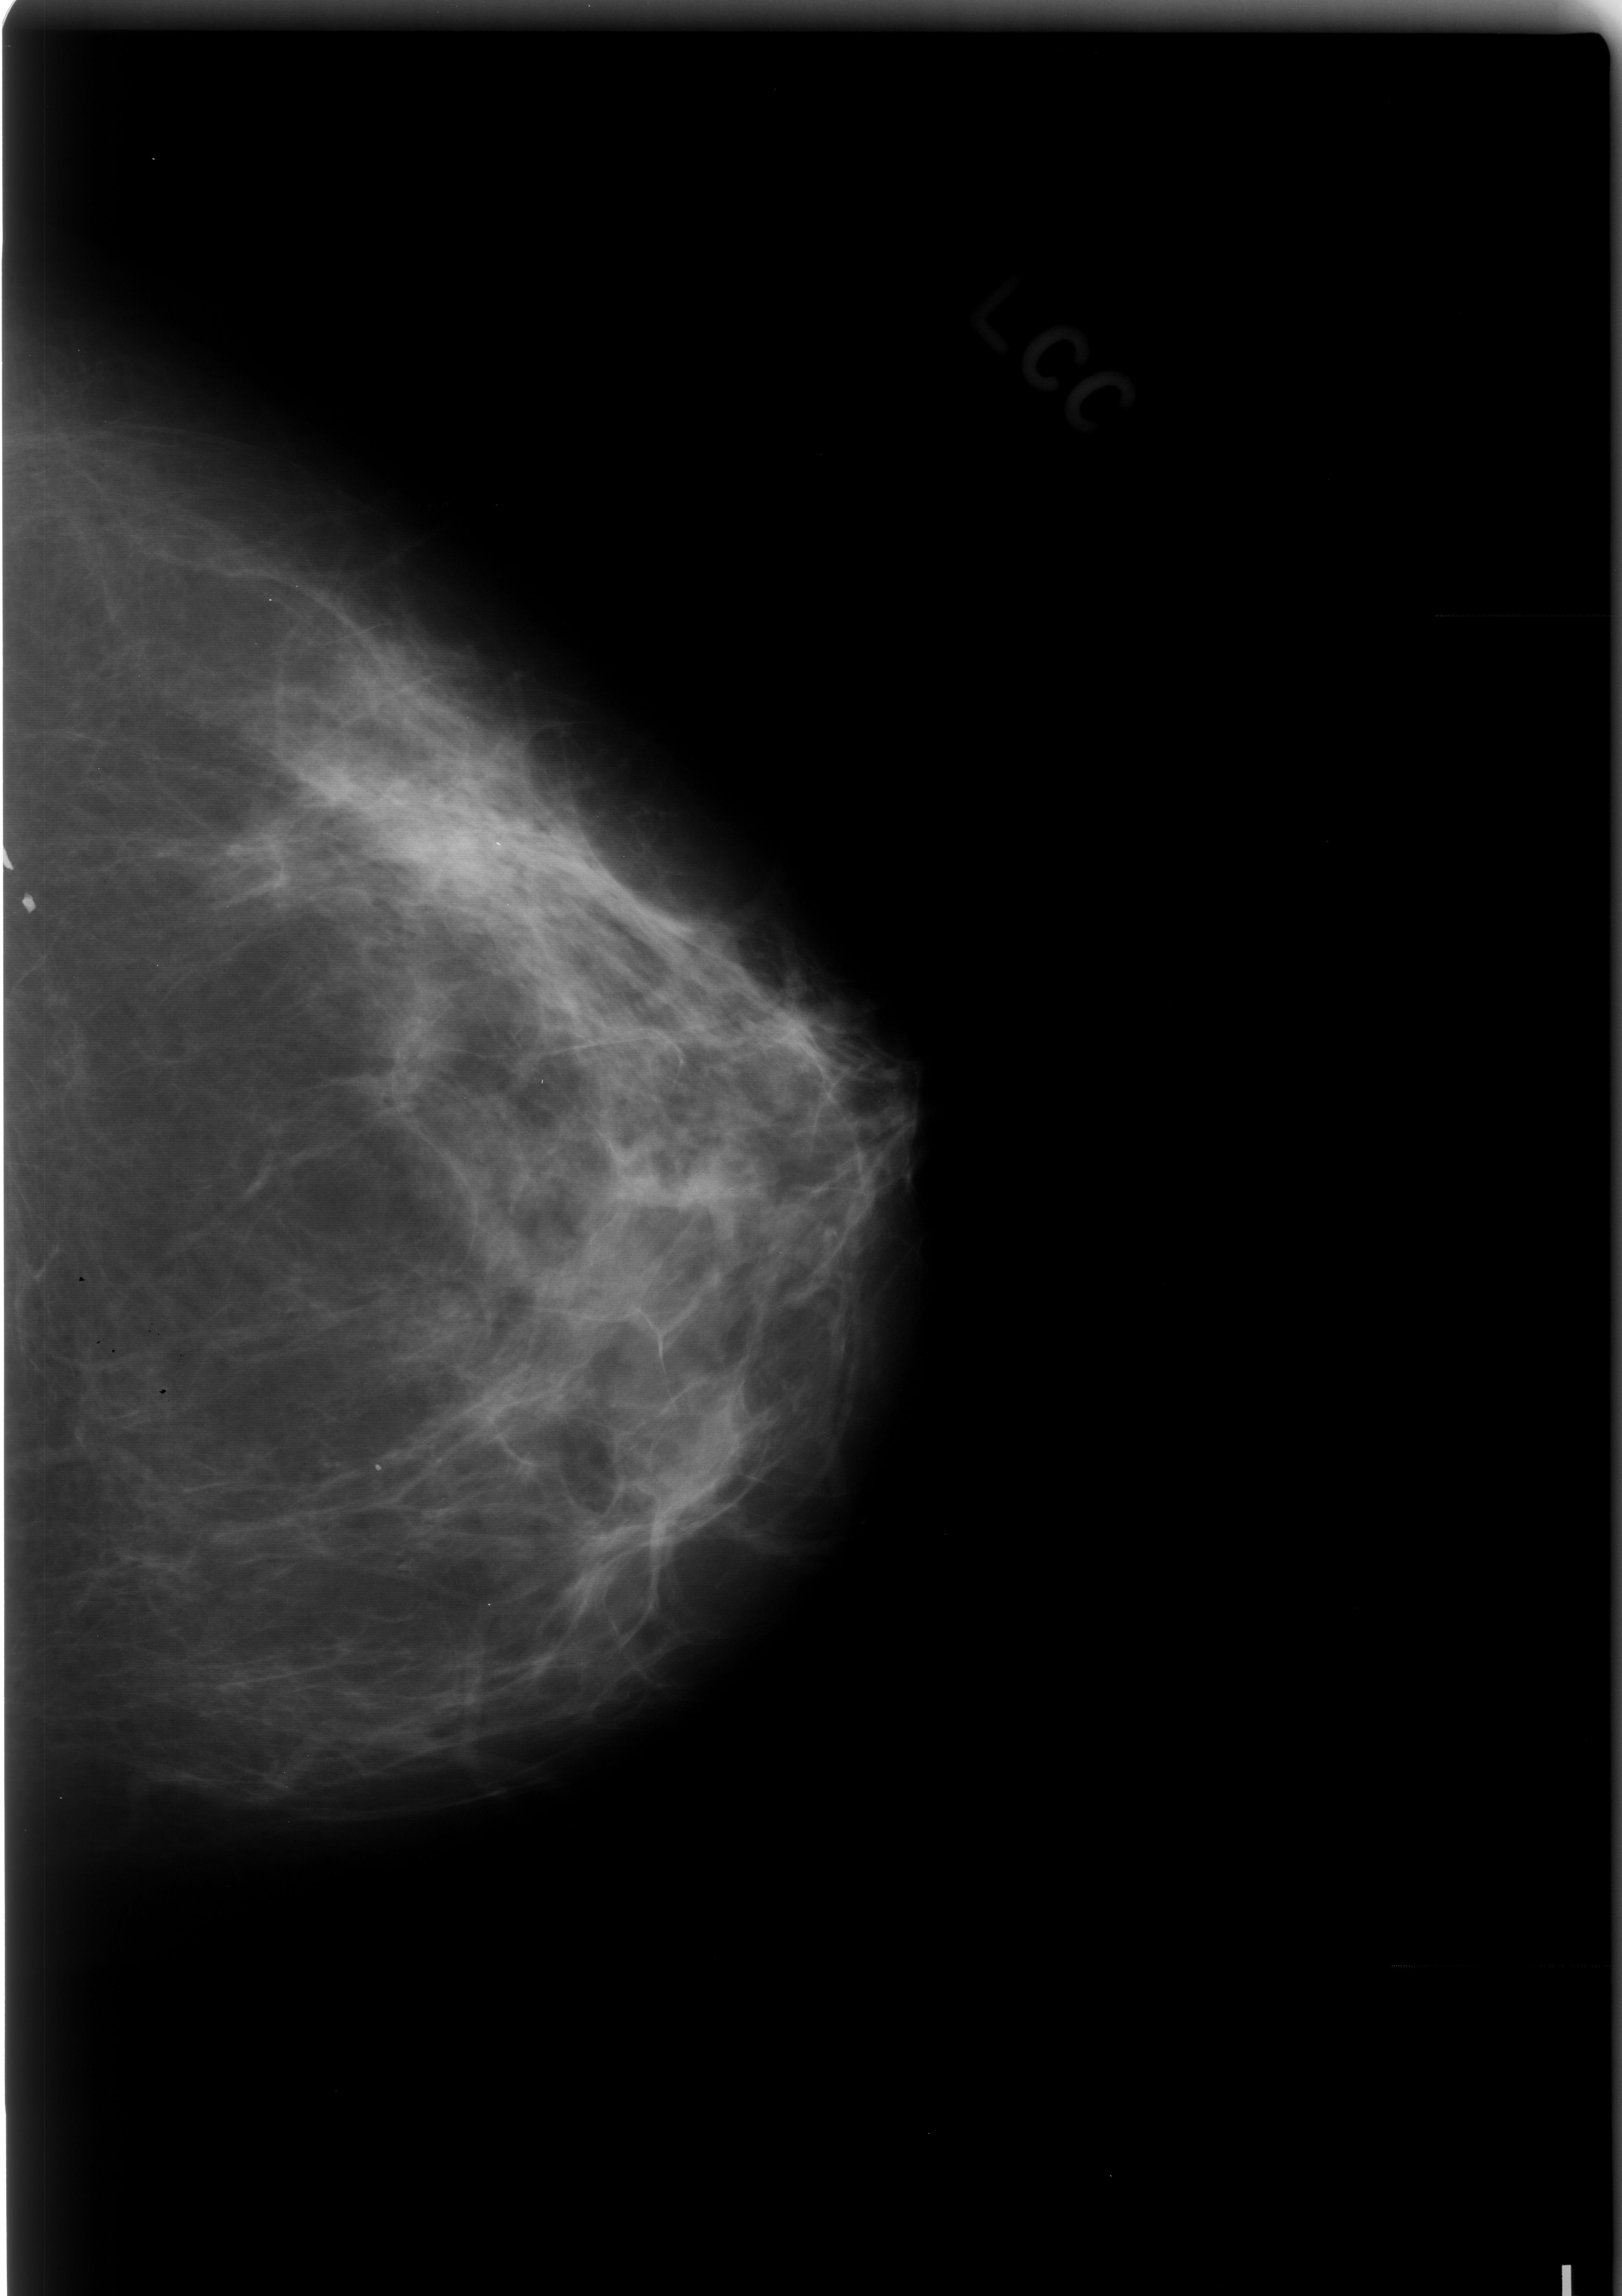
Digitized screen-film mammogram. Left breast. CC view. BI-RADS breast density category 2 (scale 1–4). 1622 × 2296 image matrix.
Marked abnormalities (boxes around the expert regions of interest):
- calcifications, morphology lucent centered, distribution linear; BI-RADS assessment category 2; subtlety rating 5 on a 1 (subtle) to 5 (obvious) scale; pathology (as recorded): benign: bounding box <3,780,97,948> (left, top, right, bottom; pixels)